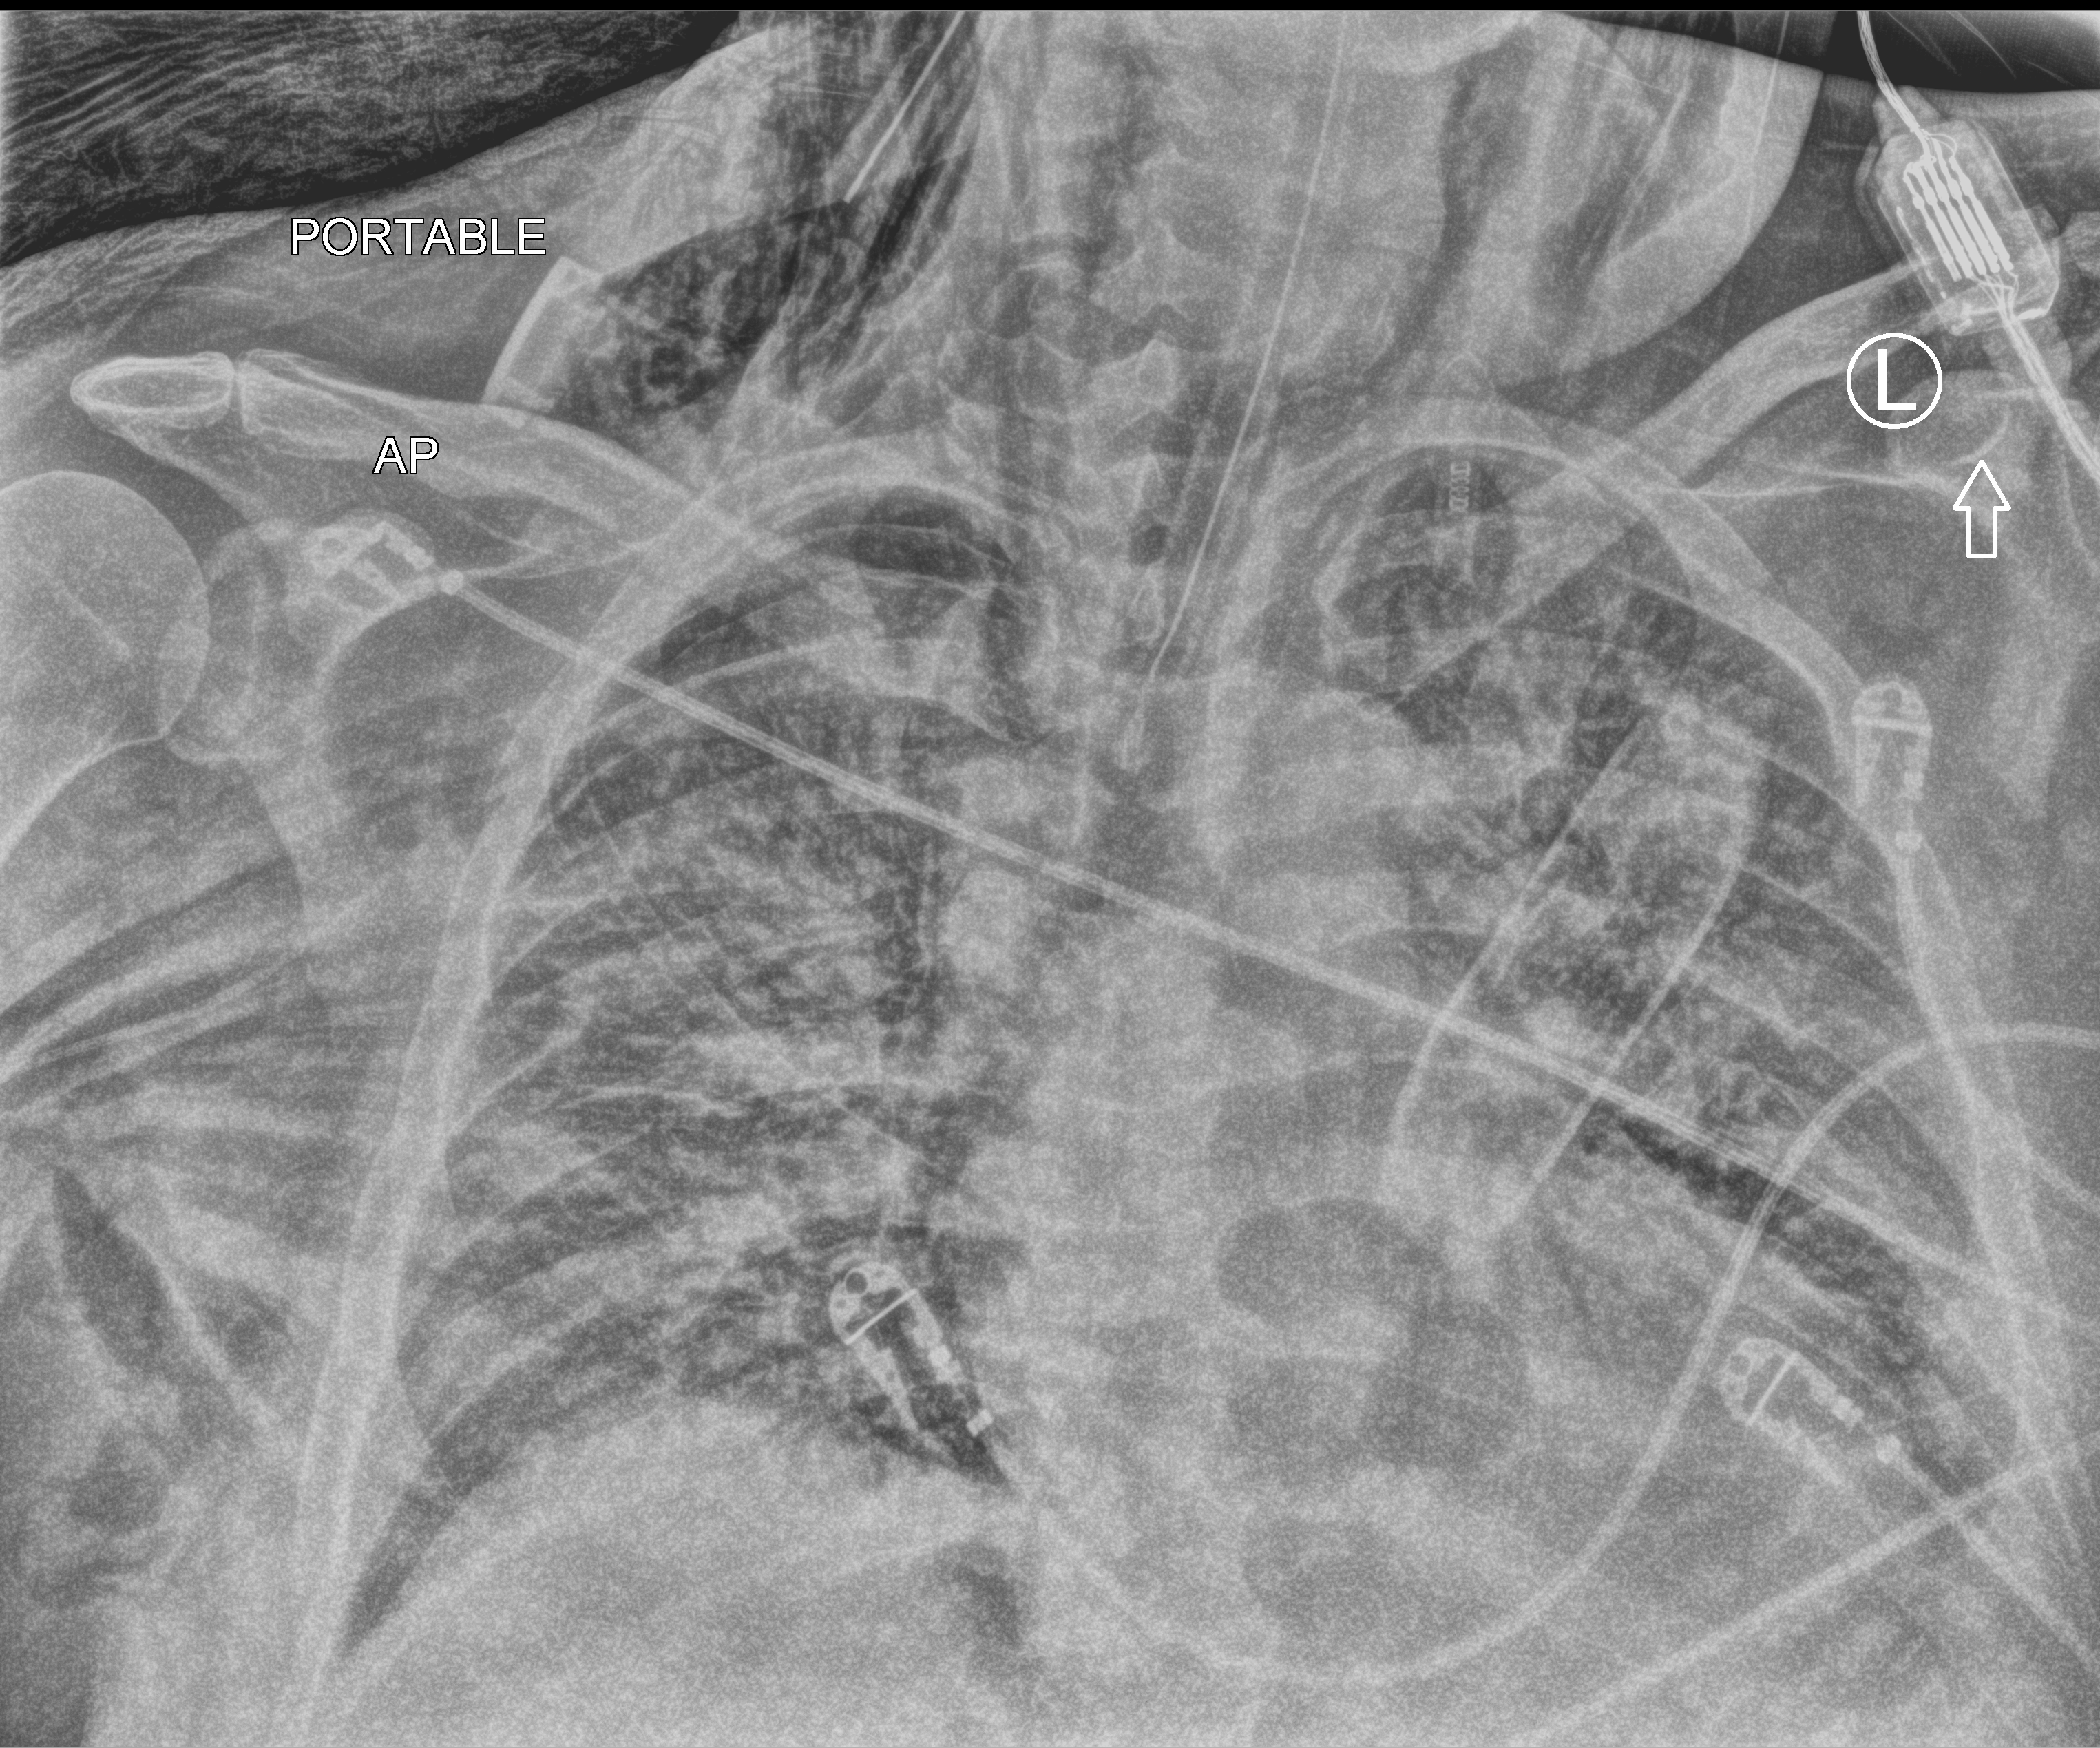
Chest X-ray (portable). Patient hospitalised with COVID-19, aged 18–59 years.
From the hospital-stay record, not from the radiograph (when in the stay this image was taken is not recorded): mechanically ventilated during this hospital stay: yes; admitted to intensive care during this hospital stay: yes.